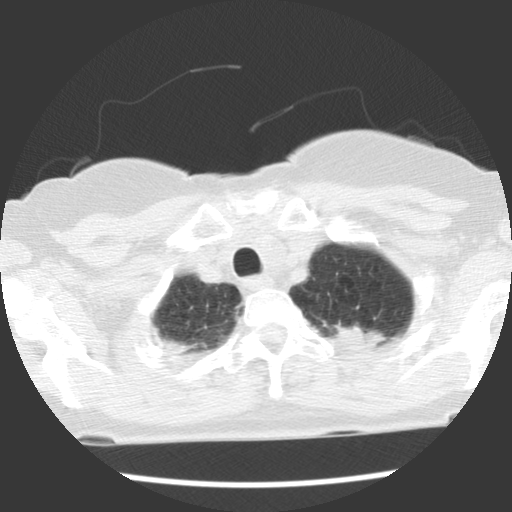
Axial slice from a low-dose chest CT screening exam. Baseline annual screen. Lung window (W 1500 / L -600 HU). Standard (soft-tissue) reconstruction kernel (STANDARD). 140 kVp. Slice 104 of 120 in the series. Female, age 66 years at enrolment. Former smoker at enrolment.
- Expert-annotated lung lesion, bounding box <316,302,385,359> (left, top, right, bottom; pixels).
- Screening reader's record for this exam (one nodule recorded; not confirmed to be the boxed lesion): non-calcified nodule or mass ≥4 mm, left upper lobe, 22 × 17 mm, spiculated (stellate) margins, soft tissue attenuation.
- Official screen result: positive, change unspecified: nodule(s) >= 4 mm or enlarging nodule(s), mass(es), or other non-specific abnormalities suspicious for lung cancer.